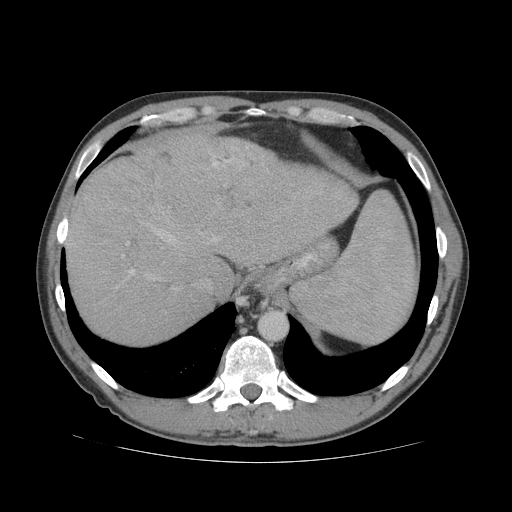
Contrast-enhanced abdominal CT (liver protocol), one axial slice. Slice 58 of 81 in the series (ordered by position). Reconstruction kernel STANDARD. Soft-tissue window (W 400 / L 40 HU). 2.5 mm slice thickness. 512 × 512 image matrix, field of view 400 × 400 mm. From the clinical record (not read from this slice): diagnosis: hepatocellular carcinoma (patient treated with transarterial chemoembolisation; whether this scan precedes or follows treatment is not stated here); TNM stage (as recorded): Stage-IVB; Child-Pugh class: B; tumour differentiation: well differentiated; tumour nodularity: multinodular.
Annotated regions visible in this slice (semi-automatically segmented with operator editing):
- abdominal aorta: bounding box <259,313,286,339> (left, top, right, bottom; pixels)
- liver parenchyma outside the tumour (the mass and vessels are separate outlines, so this box may not span the whole liver): <66,132,358,344>
- mass: <82,136,270,234>
- liver vessels: <127,228,218,280>